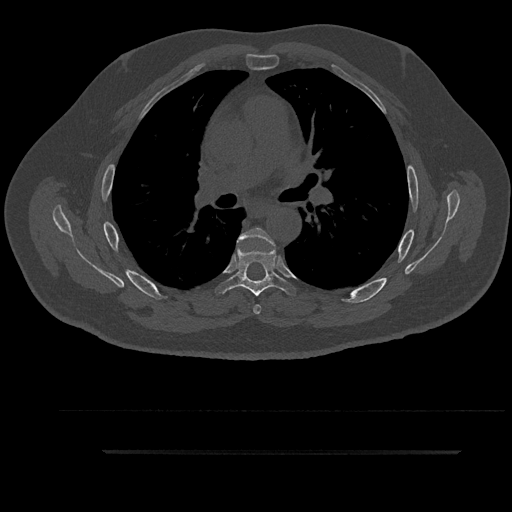
CT including the spine, one axial slice; bone window (W 1800 / L 400 HU); 512 × 512 image matrix, field of view 432 × 432 mm. Male patient, age 63 years. From the clinical record (not read from this slice): primary cancer: renal.
Structures marked on this image (semi-automatically segmented with operator editing):
- T5 vertebra: bounding box <237,227,275,314> (left, top, right, bottom; pixels)
- T6 vertebra: <219,240,289,296>